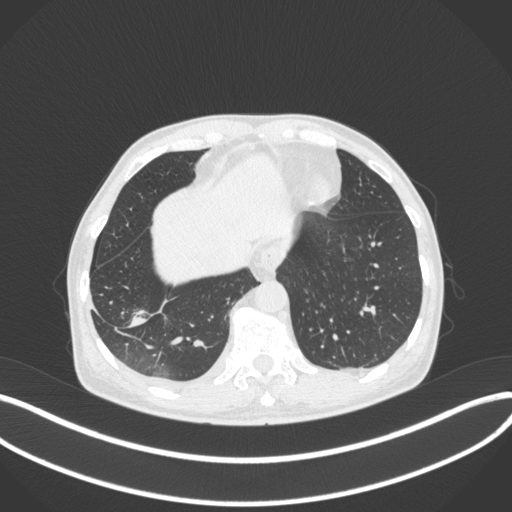
Chest CT, one axial slice; reconstruction kernel B31f; 120 kVp; lung window (W 1500 / L -600 HU); 1 mm slice thickness; 512 × 512 image matrix, field of view 400 × 400 mm. Male patient, age 64 years. Case-level facts recorded for this patient, not image findings: clinical TNM (as recorded): T3 N0 M0.
Annotated regions visible in this slice (rectangle marked by the reading radiologist):
- lung tumour (recorded histology: adenocarcinoma): bounding box <130,307,151,332> (left, top, right, bottom; pixels)